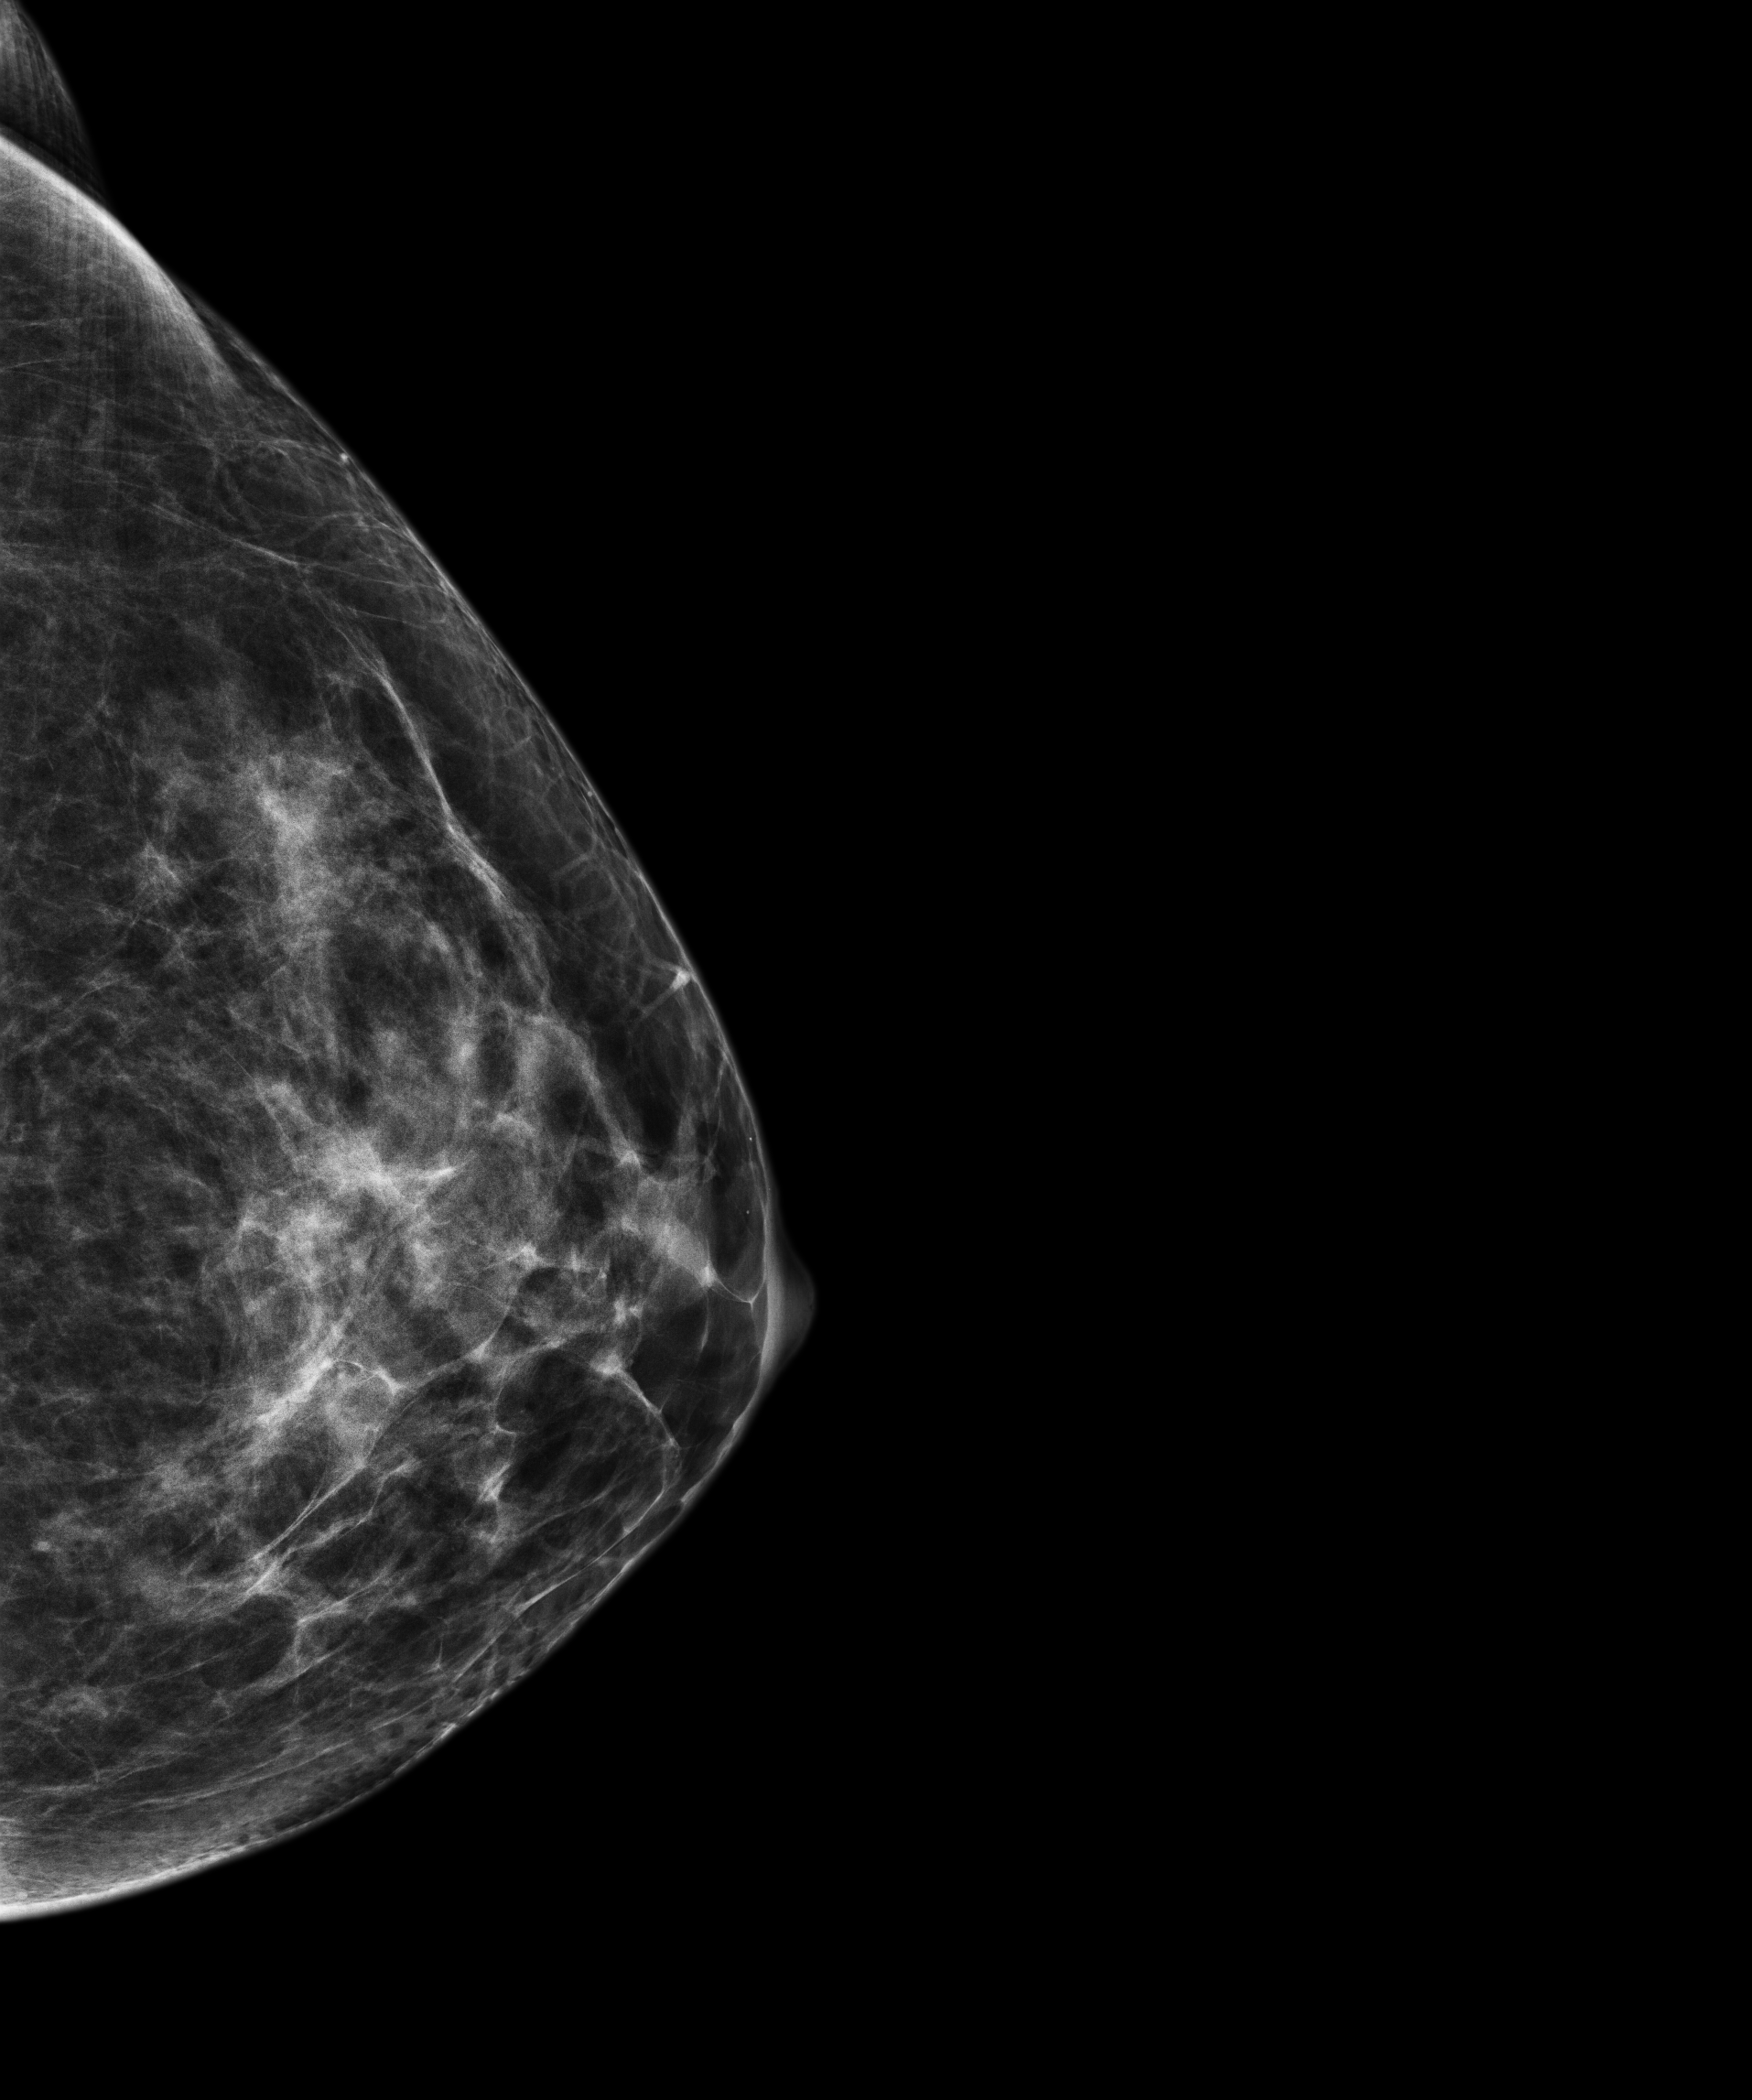
Annual screening mammography examination, system: Senographe Pristina. Patient: female, 44 years.
Image type: full-field digital mammogram. Breast: left. Projection: CC view.